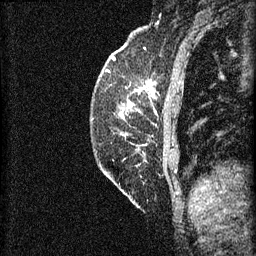
Breast MRI (dynamic contrast-enhanced), one sagittal slice; slice 18 of 60 in the series (ordered by position); 3 images stored at this slice position (order not interpretable as contrast timing); 1.5 T; TE 4.2 ms, TR 8.2 ms; 2 mm slice thickness; 256 × 256 image matrix, field of view 180 × 180 mm. Patient: female, 59 years.
Annotated regions visible in this slice (semi-automatically segmented with operator editing):
- analysis volume of interest (the breast-tissue region the enhancement analysis was run in; not a lesion): box from (x=99, y=76) to (x=155, y=121) px
- tumour enhancement mask (voxels above the 70 % enhancement threshold inside the analysis volume of interest): (x=128, y=88)–(x=154, y=109)